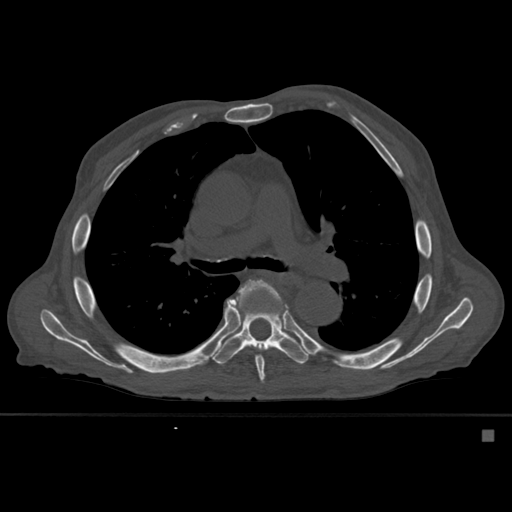
CT including the spine, one axial slice. Slice 375 of 527 in the series (ordered by position). Bone window (W 1800 / L 400 HU). 1.5 mm slice thickness. 512 × 512 image matrix, field of view 373 × 373 mm. Patient: male, 78 years. Case-level facts recorded for this patient, not image findings: primary cancer: prostate.
Outlined on this slice (semi-automatically segmented with operator editing):
- T6 vertebra: box from (x=229, y=279) to (x=279, y=384) px
- T7 vertebra: (x=213, y=289)–(x=309, y=365)